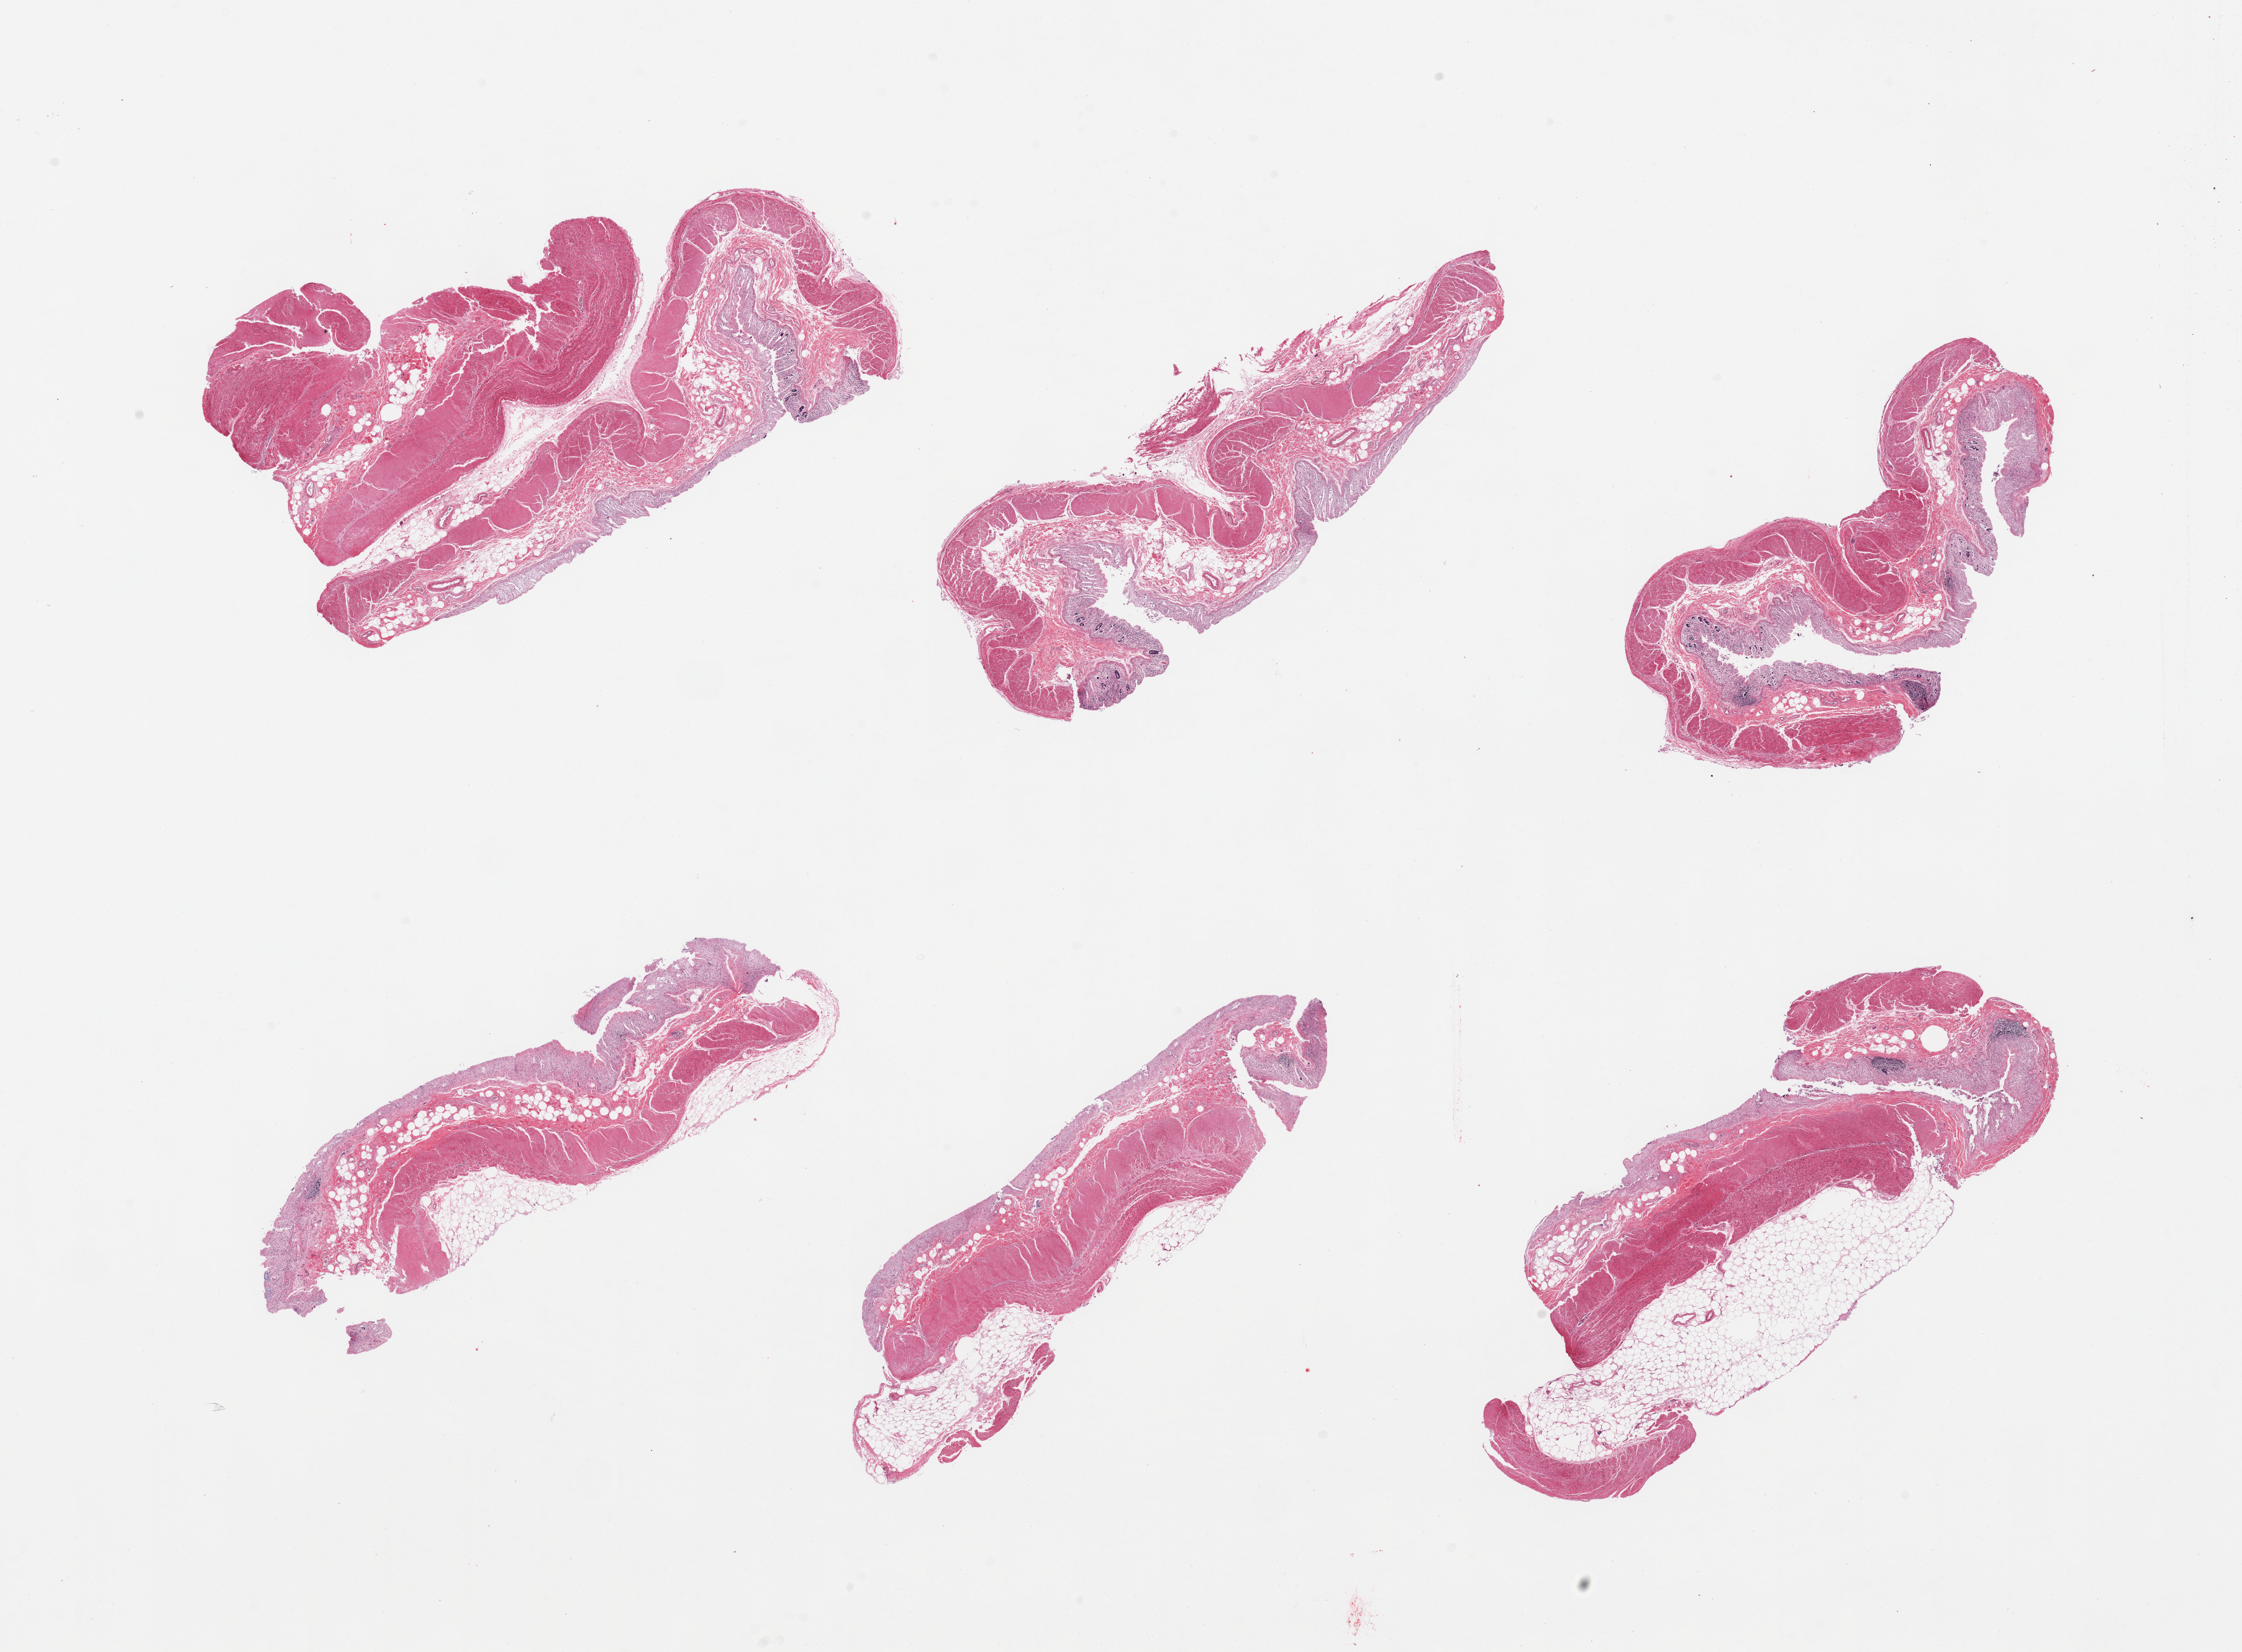
Digitized hematoxylin and eosin (H&E)-stained section, a low-resolution overview of the entire scanned area, about 28.5 x 21.0 mm. PAXgene-fixed paraffin-embedded (PFPE) section. Sampled site (target tissue): transverse colon. Donor tissue sample. Donor: male.
Reviewer comment on this tissue sample: 6 pieces, mucosa completely autolyzed/sloughted.